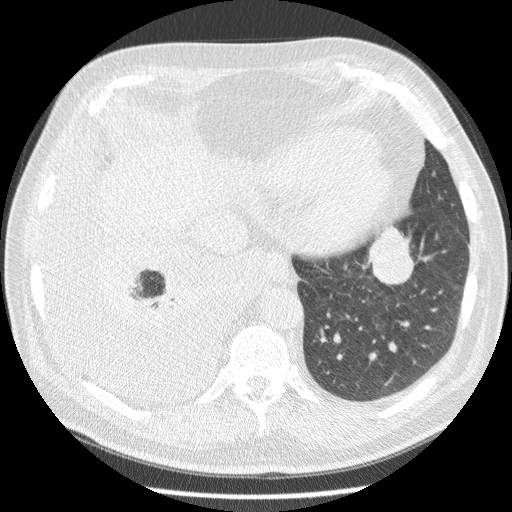
Chest CT (low-dose screening protocol), one axial image. Third annual screen. Lung window (W 1500 / L -600 HU). Male, age 63 years at enrolment. Current smoker at enrolment.
Expert reader's lesion annotation, box from (x=356, y=219) to (x=420, y=286) px. Screening reader's record for this exam (one nodule recorded; not confirmed to be the boxed lesion): non-calcified nodule or mass ≥4 mm, left lower lobe, 34 × 31 mm, smooth margins, soft tissue attenuation, pre-existing on the prior screen: yes; interval growth: yes. Official screen result: positive, other.